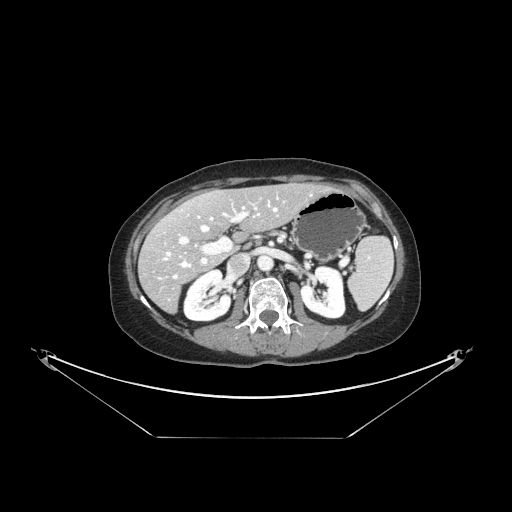
Contrast-enhanced abdominal CT, one axial slice; slice 81 of 148 in the series (ordered by position); reconstruction kernel STANDARD; soft-tissue window (W 400 / L 40 HU); 512 × 512 image matrix, field of view 500 × 500 mm. Female patient, age 73 years. From the clinical record (not read from this slice): diagnosis: colorectal cancer liver metastases, imaged before liver resection; multiple liver metastases: no; largest metastasis: 1 cm.
Annotated regions visible in this slice (outlined manually by an expert reader):
- hepatic veins: bounding box (x1, y1, x2, y2) in pixels: (164, 203, 278, 278)
- liver: (139, 184, 327, 312)
- planned liver remnant (the part of the liver to remain after resection): (168, 184, 326, 238)
- portal vein (with intrahepatic branches): (179, 204, 257, 264)